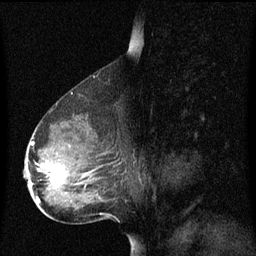
Breast MRI (dynamic contrast-enhanced), one sagittal slice. Position 40 of 60 along the scan axis. Dynamic contrast-enhanced series, image 2 of 3 at this slice position (ordered by acquisition). 1.5 T. TE 4.2 ms, TR 8.4 ms. 256 × 256 image matrix, field of view 200 × 200 mm. Patient: female, 49 years. Case-level facts recorded for this patient, not image findings: setting: breast cancer imaged before/during neoadjuvant chemotherapy; receptor status: HR-positive, HER2-negative.
Annotated regions visible in this slice (semi-automatically segmented with operator editing):
- analysis volume of interest (the breast-tissue region the enhancement analysis was run in; not a lesion): box from (x=25, y=126) to (x=121, y=201) px
- tumour enhancement mask (voxels above the 70 % enhancement threshold inside the analysis volume of interest): (x=30, y=142)–(x=68, y=201)